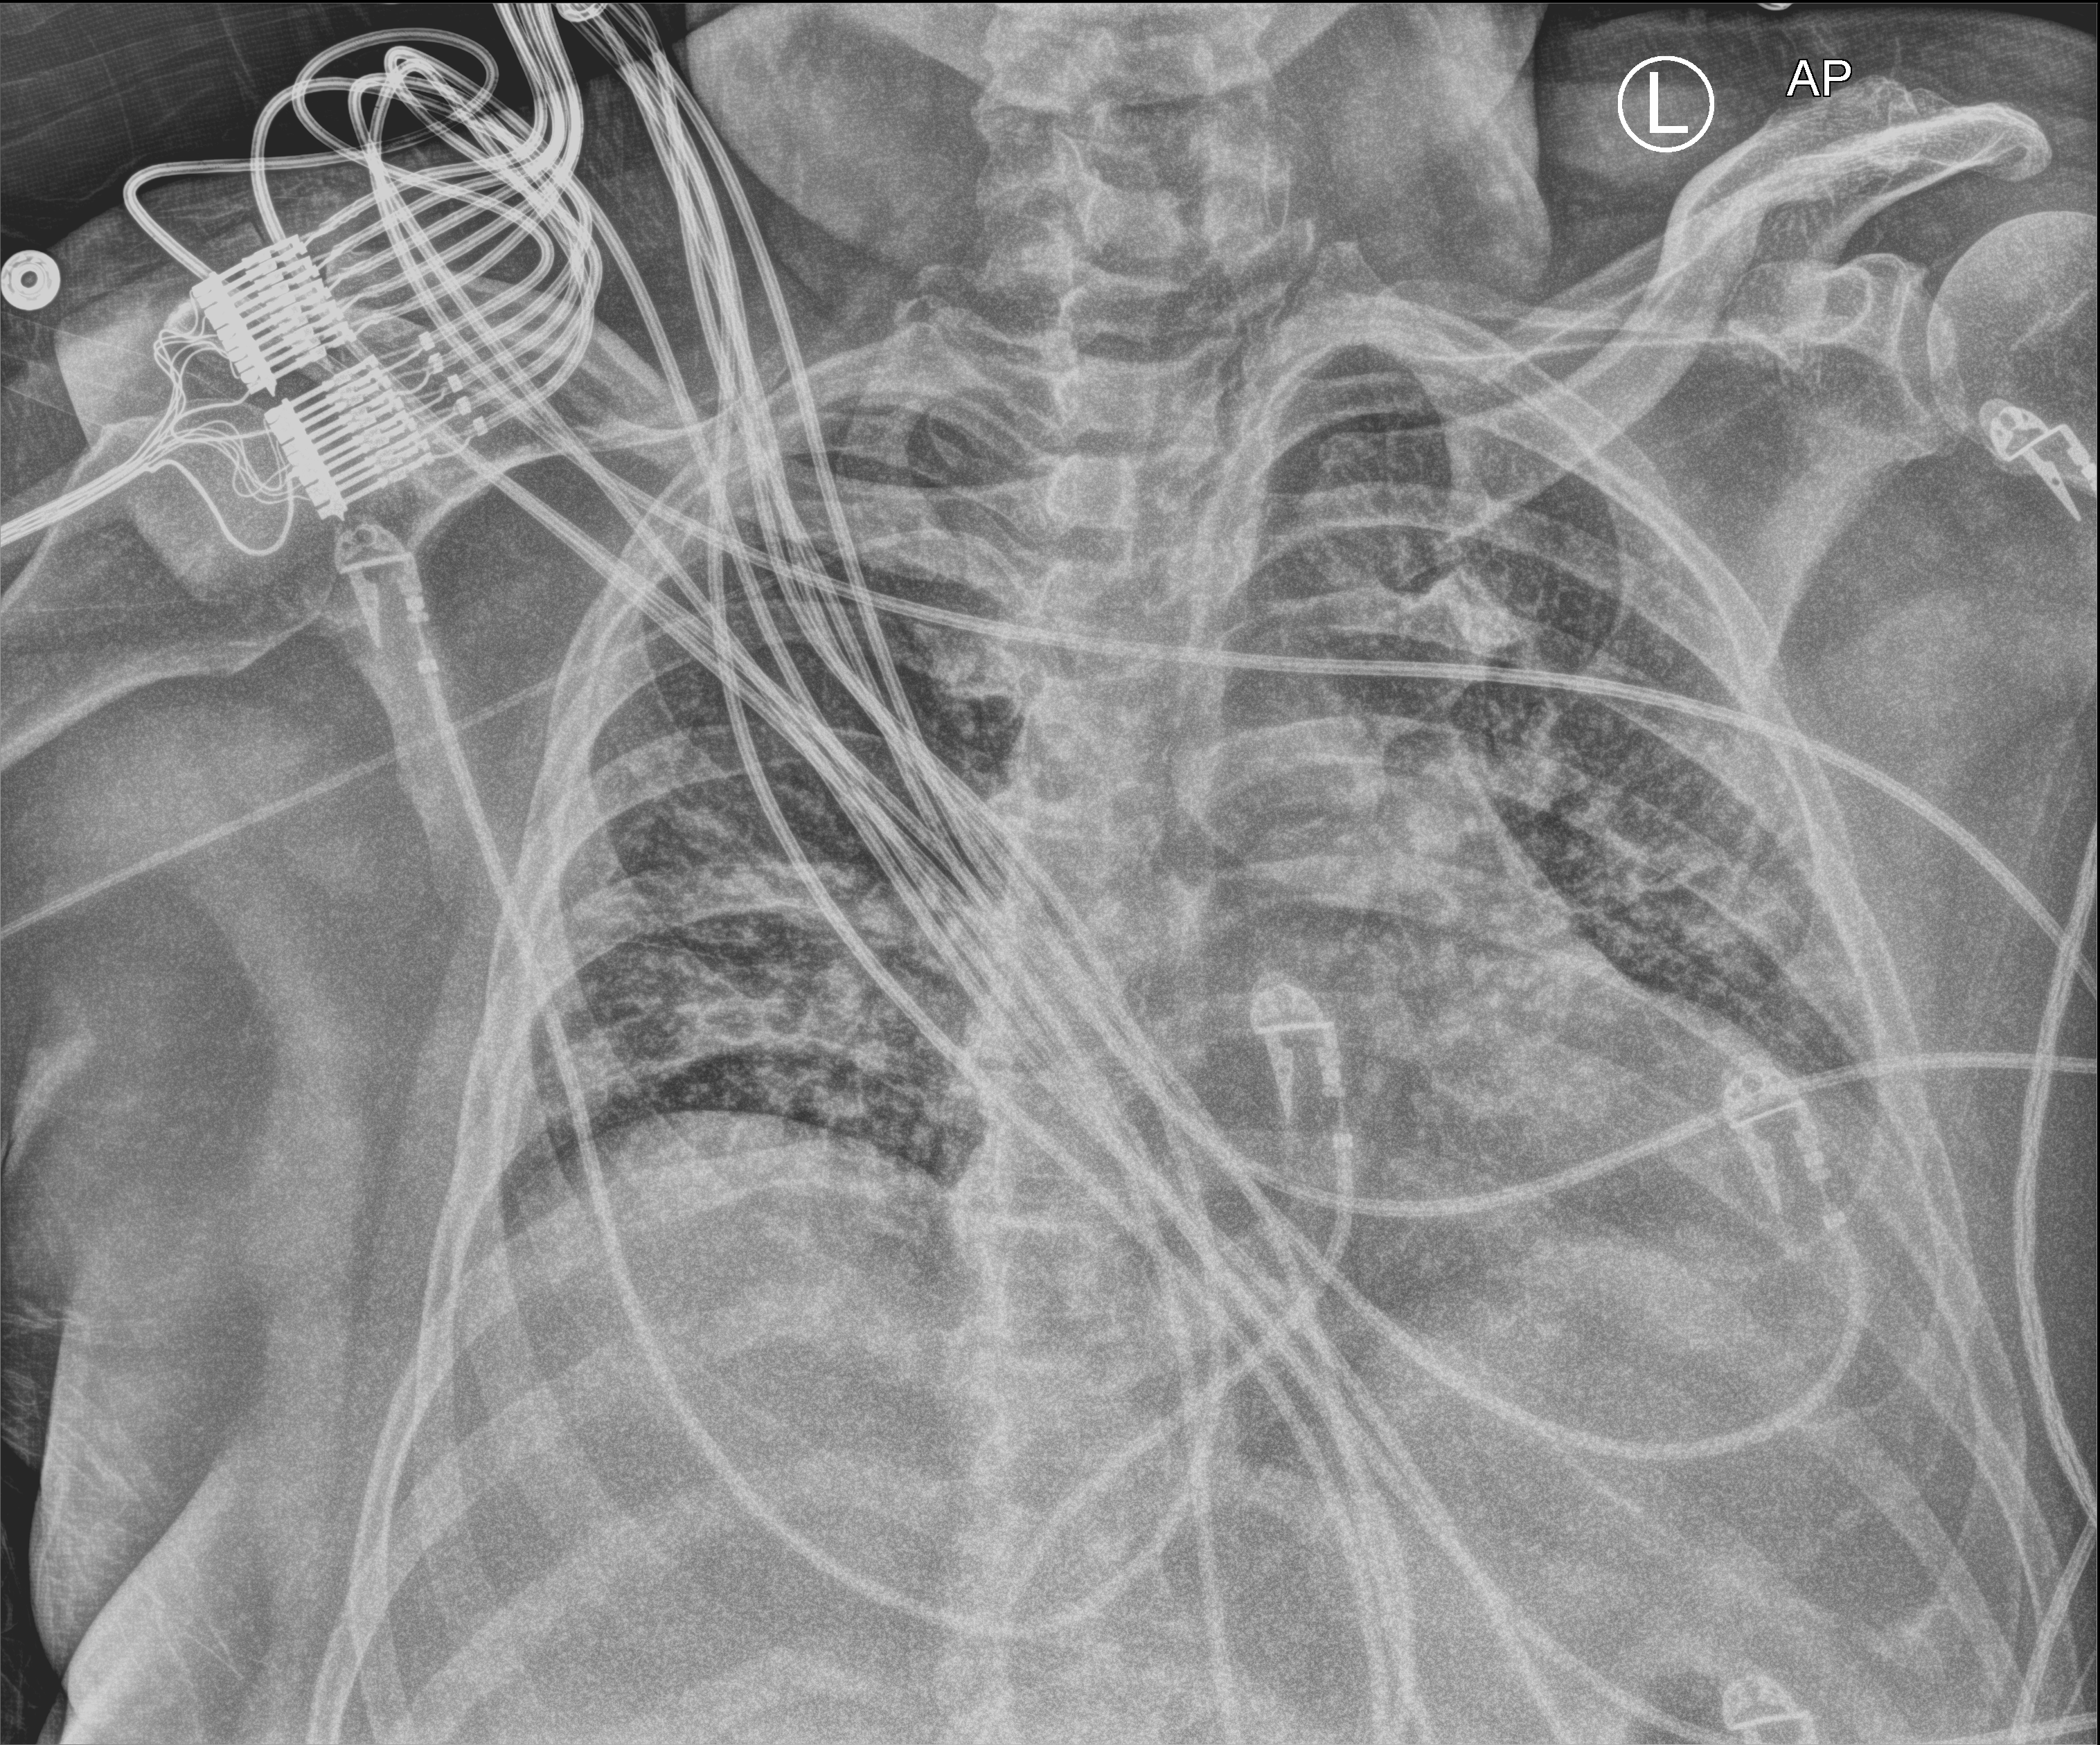
Portable chest radiograph, anteroposterior (AP) projection. Patient hospitalised with COVID-19; male, aged 18–59 years.
From the hospital-stay record, not from the radiograph (when in the stay this image was taken is not recorded): admitted to intensive care during this hospital stay: yes.